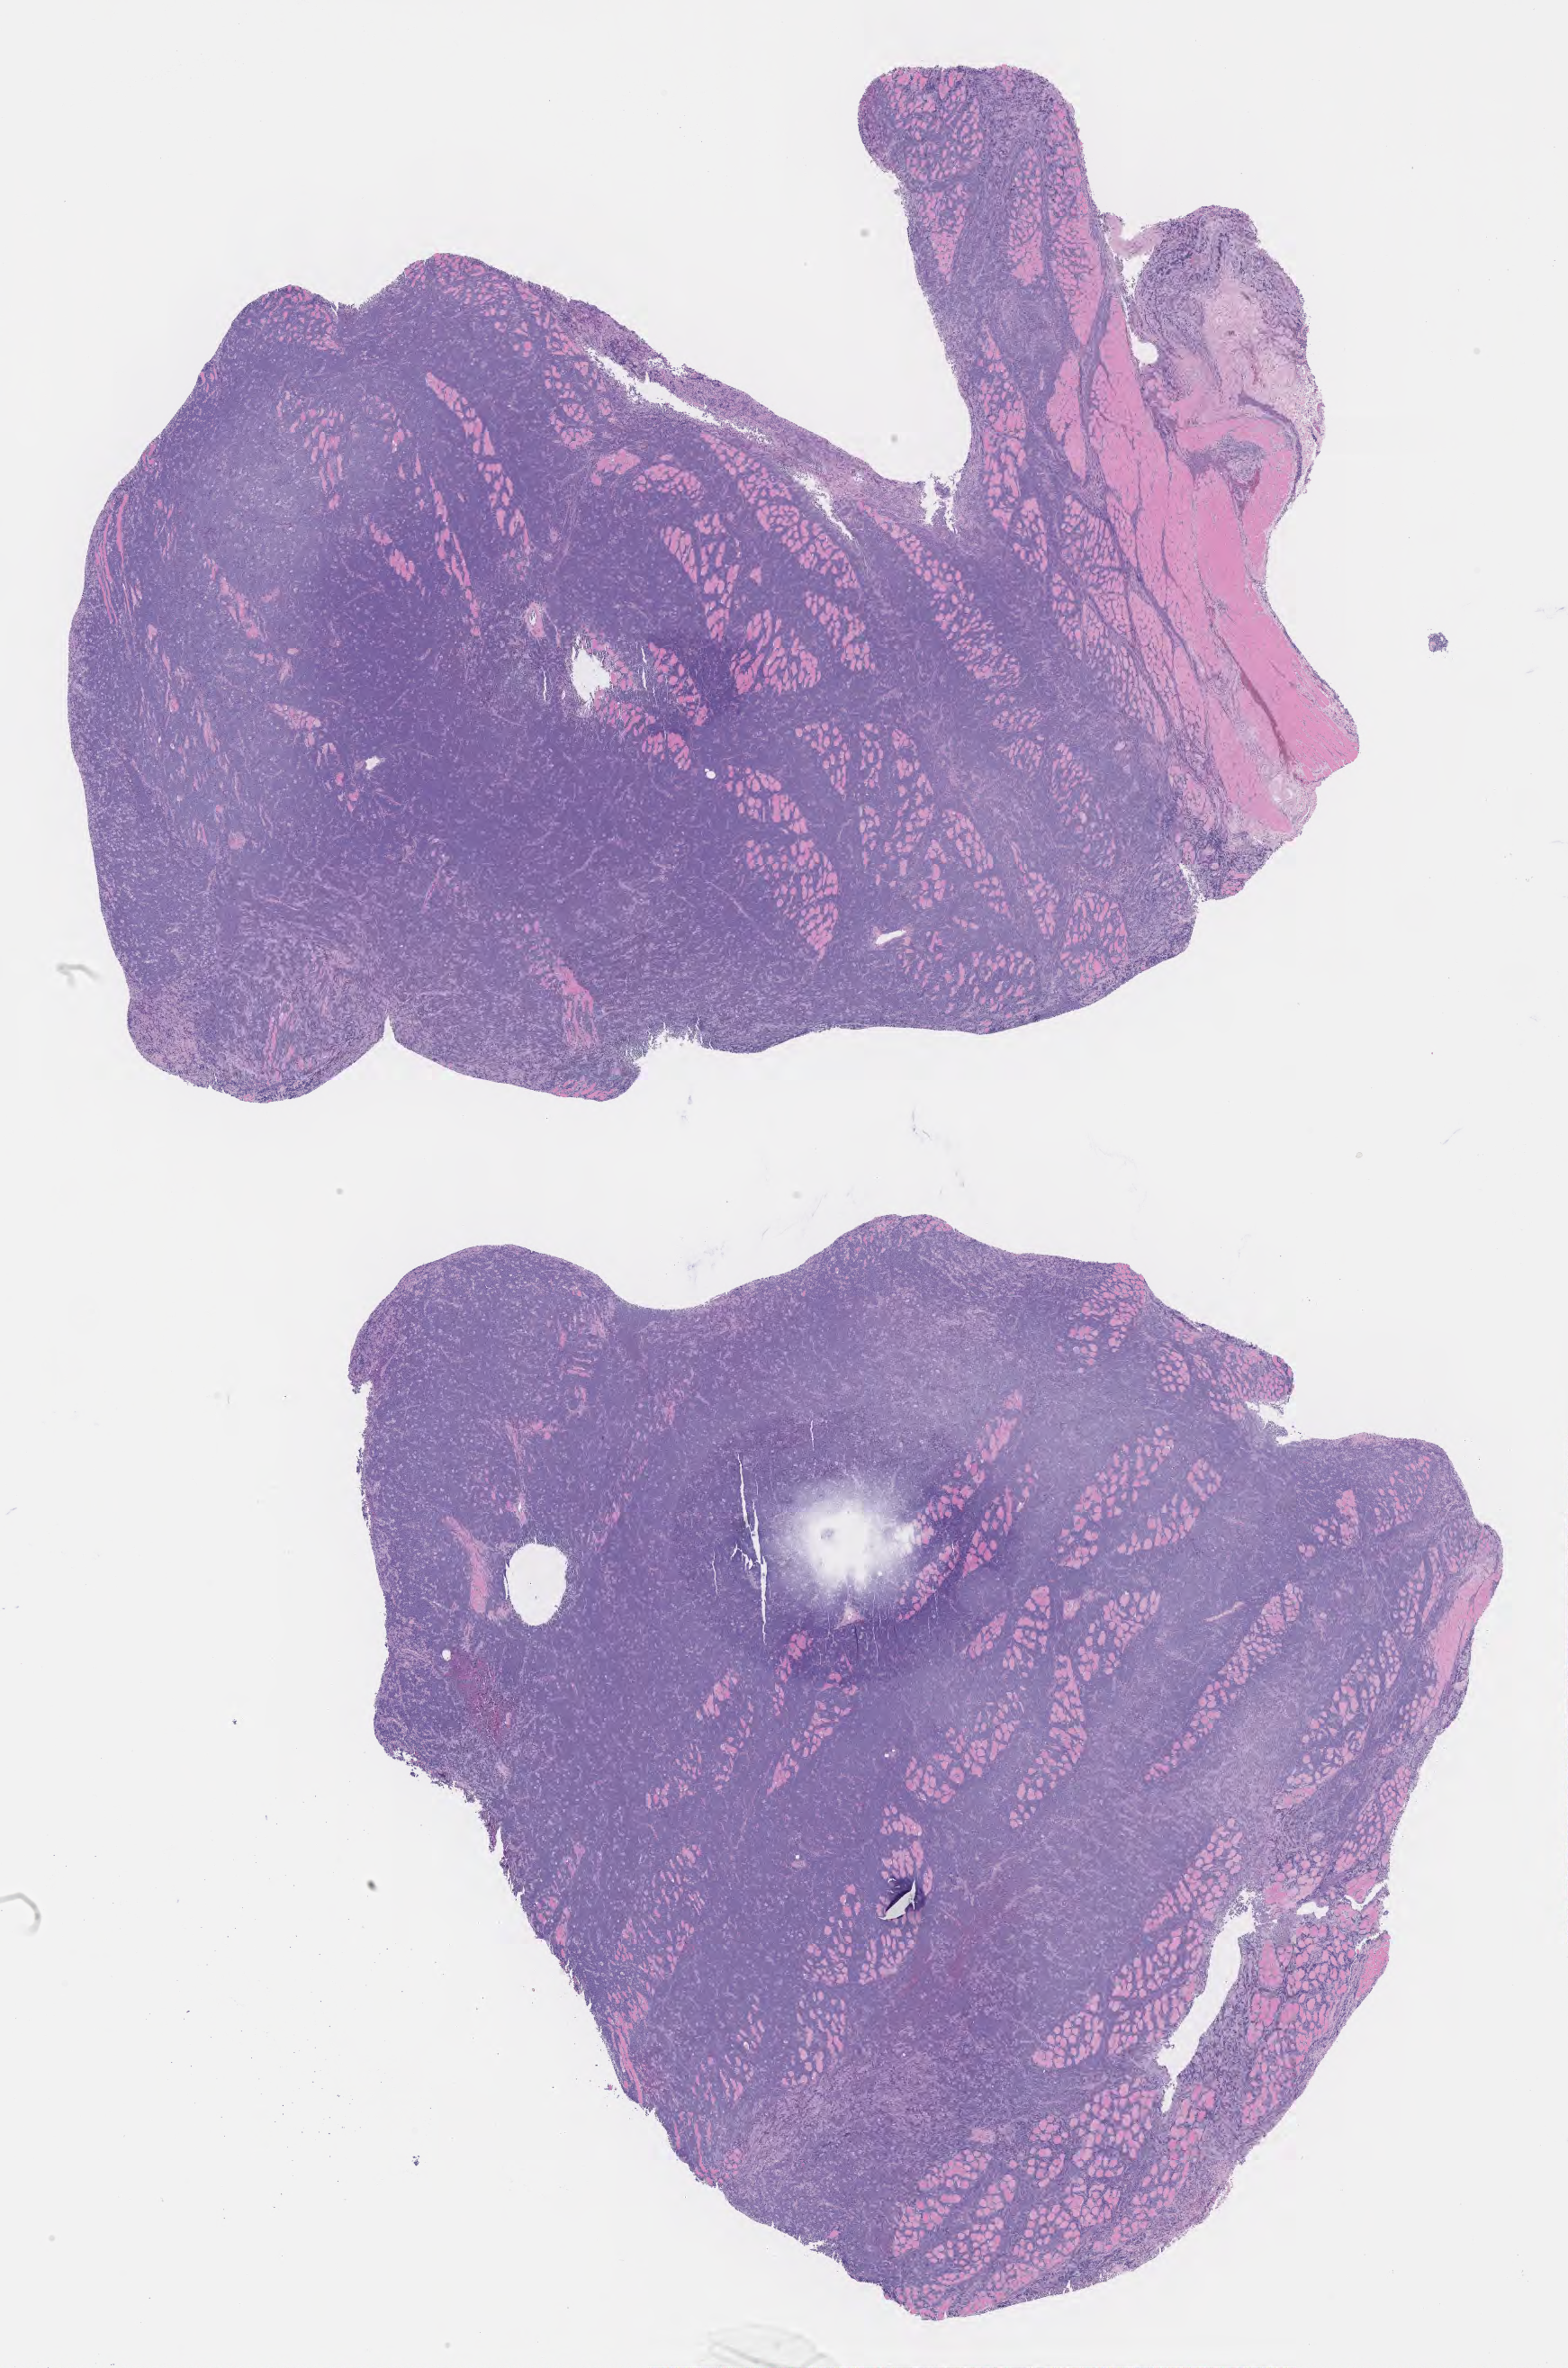
Digitized hematoxylin and eosin (H&E)-stained section — low-resolution overview of the scanned area, about 14.1 x 21.3 mm, tumor tissue, site: head and neck. Patient: male, 53 years old.
Histologic diagnosis: Burkitt lymphoma, NOS.